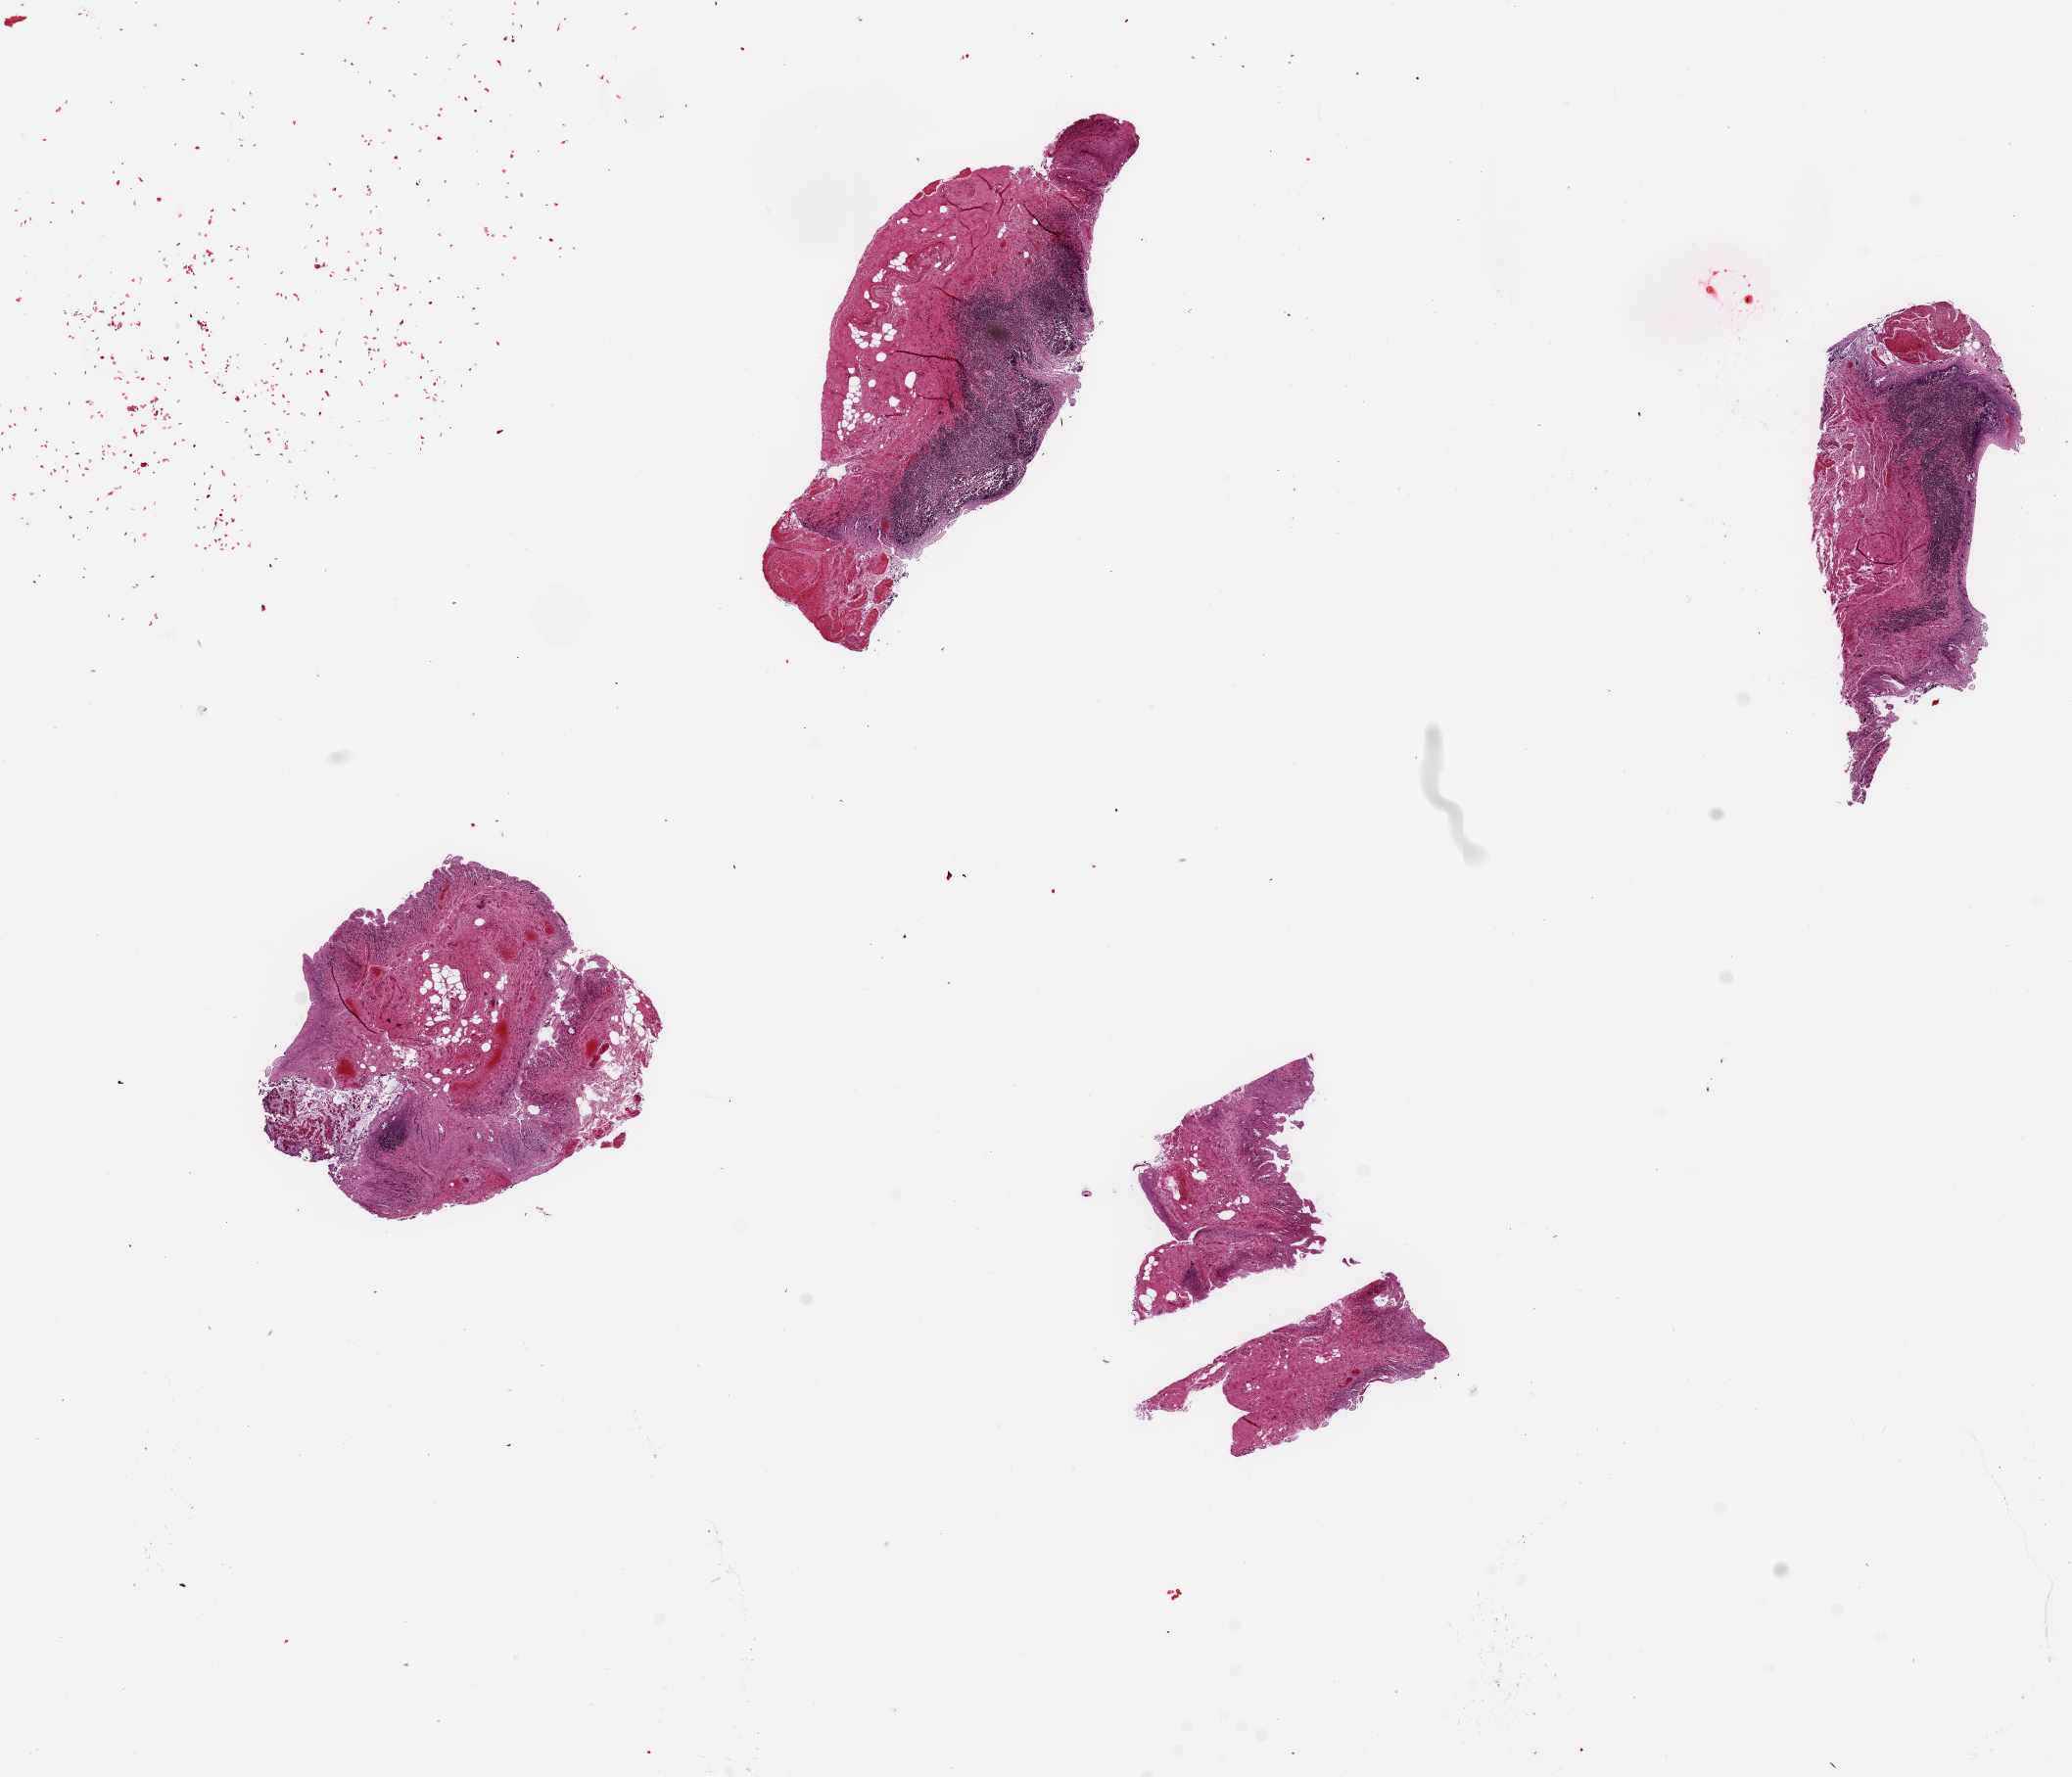
Whole-slide image, hematoxylin and eosin (H&E) stain, brightfield, whole scanned area (about 16.7 x 14.4 mm, slide scanned at 20x) shown as a low-resolution overview, PAXgene-fixed, paraffin-embedded tissue, target tissue: ileum, tissue donor sample.
- review note (as recorded): 4 pieces, up to 5x2mm; ~10% lymphoid aggregates, badly autolyzed